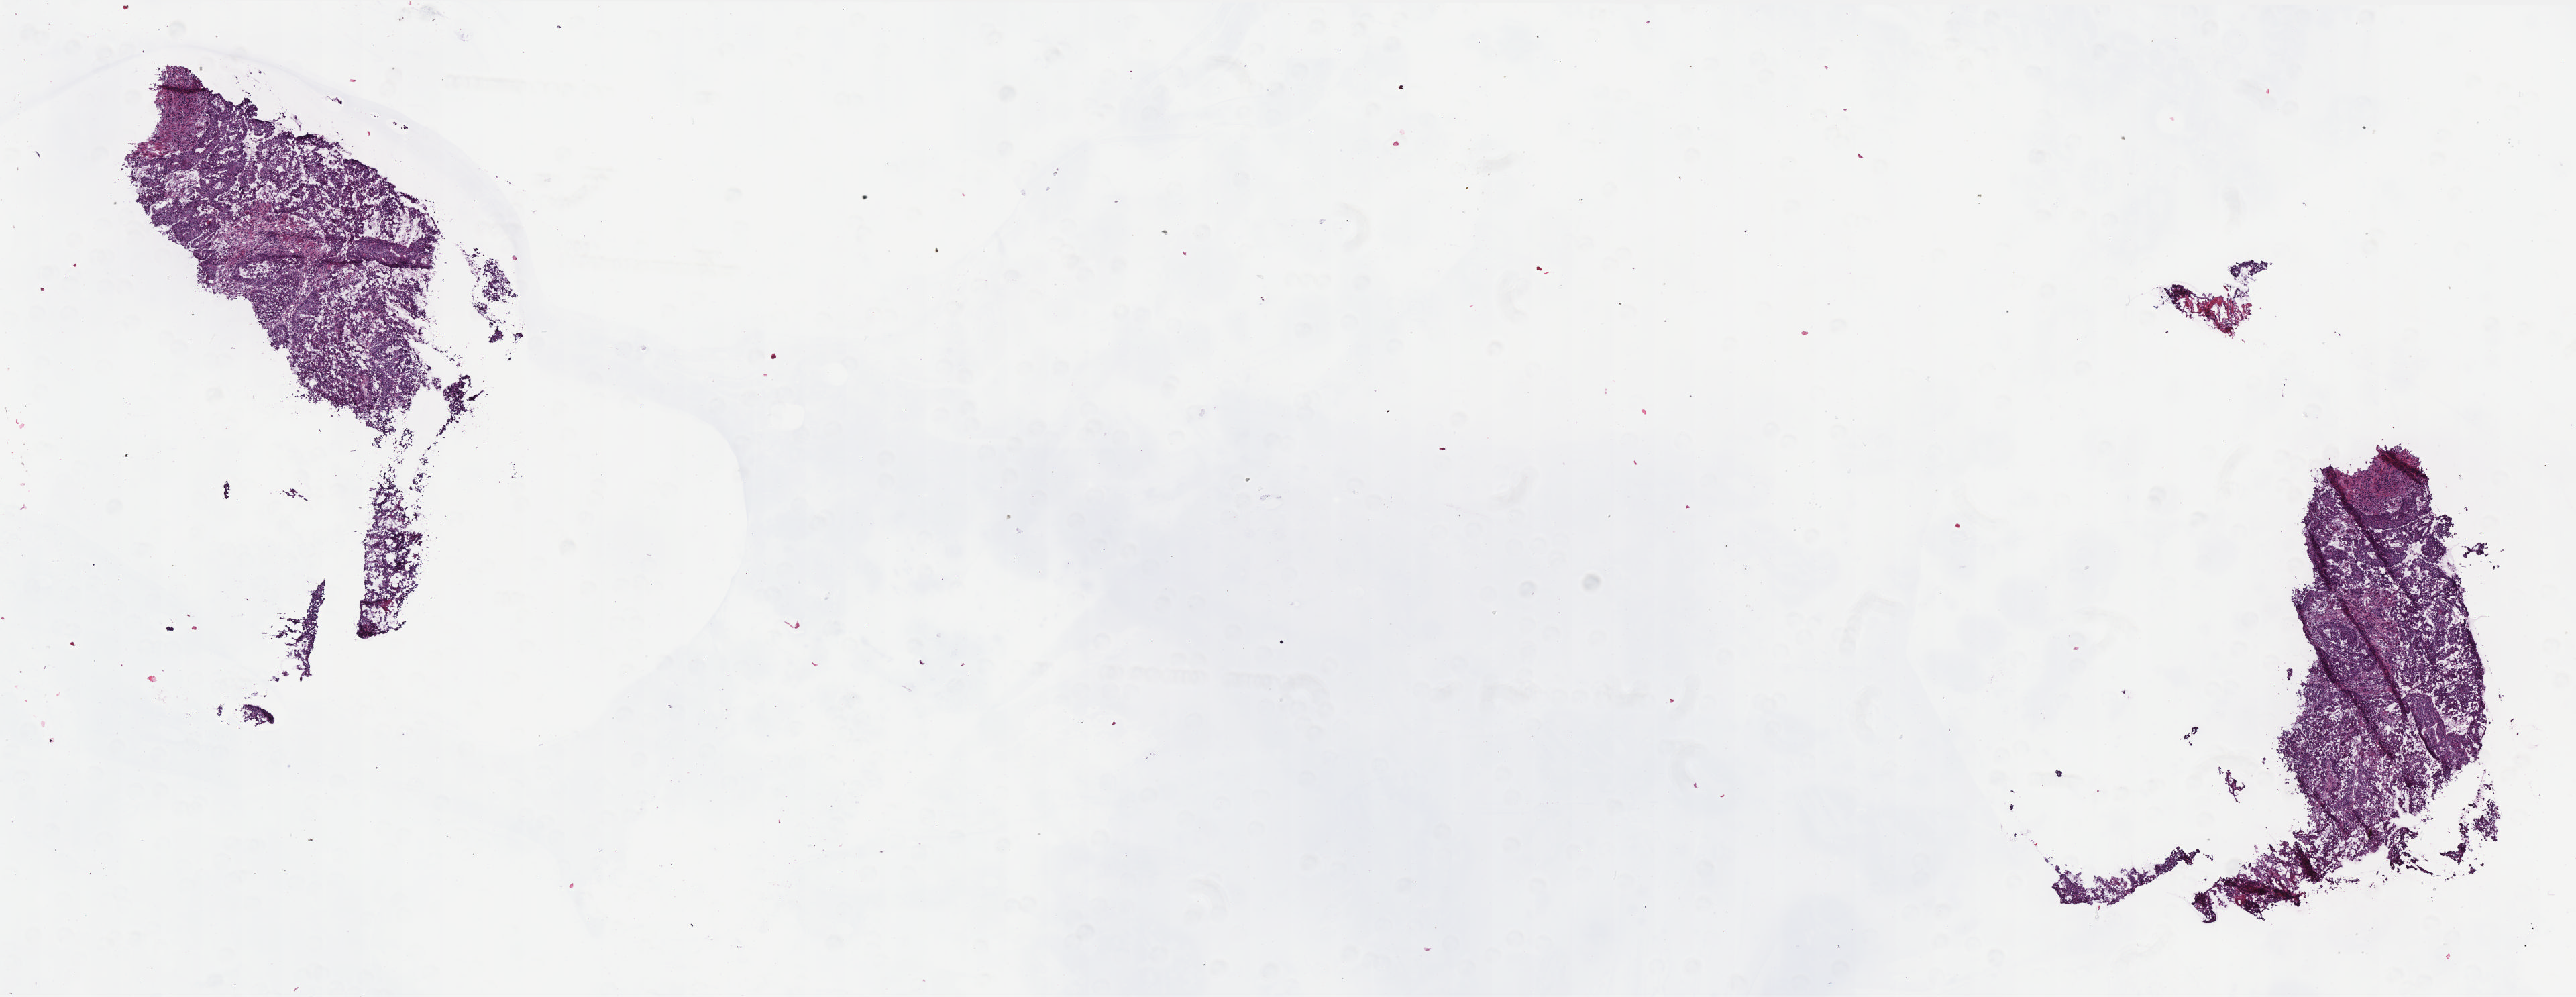
Whole-slide histology image, H&E — low-resolution overview of the scanned area, about 15.4 x 6.0 mm, frozen section, primary tumour sample from the colon. Male, age 63 years at initial diagnosis. Composition of this section per pathologist review: tumour cells 85%, tumour nuclei 85%, normal cells 0%, stromal cells 13%, necrosis 2%. Infiltration values recorded for this section: lymphocyte infiltration 4%, monocyte infiltration 4%, neutrophil infiltration 2%.
- TNM: T3 N0 M0
- lymph nodes positive (case pathology): 0 of 22 examined
- pathologic diagnosis: Mucinous adenocarcinoma (cecum)
- AJCC pathologic stage: IIA